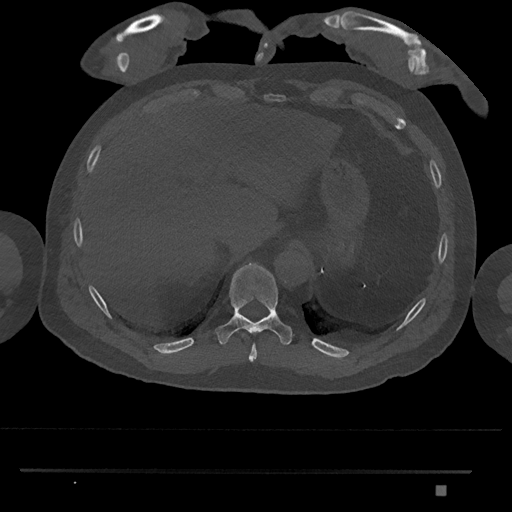
CT including the spine, one axial slice. Position 1004 of 1134 along the scan axis. 120 kVp. Bone window (W 1800 / L 400 HU). 0.5 mm slice thickness. 512 × 512 image matrix, field of view 429 × 429 mm. Patient: male, 65 years. Case-level facts recorded for this patient, not image findings: primary cancer: prostate.
Outlined on this slice (semi-automatic segmentation, software-assisted and operator-edited):
- T10 vertebra: box from (x=215, y=262) to (x=293, y=345) px
- T9 vertebra: (x=248, y=344)–(x=257, y=362)